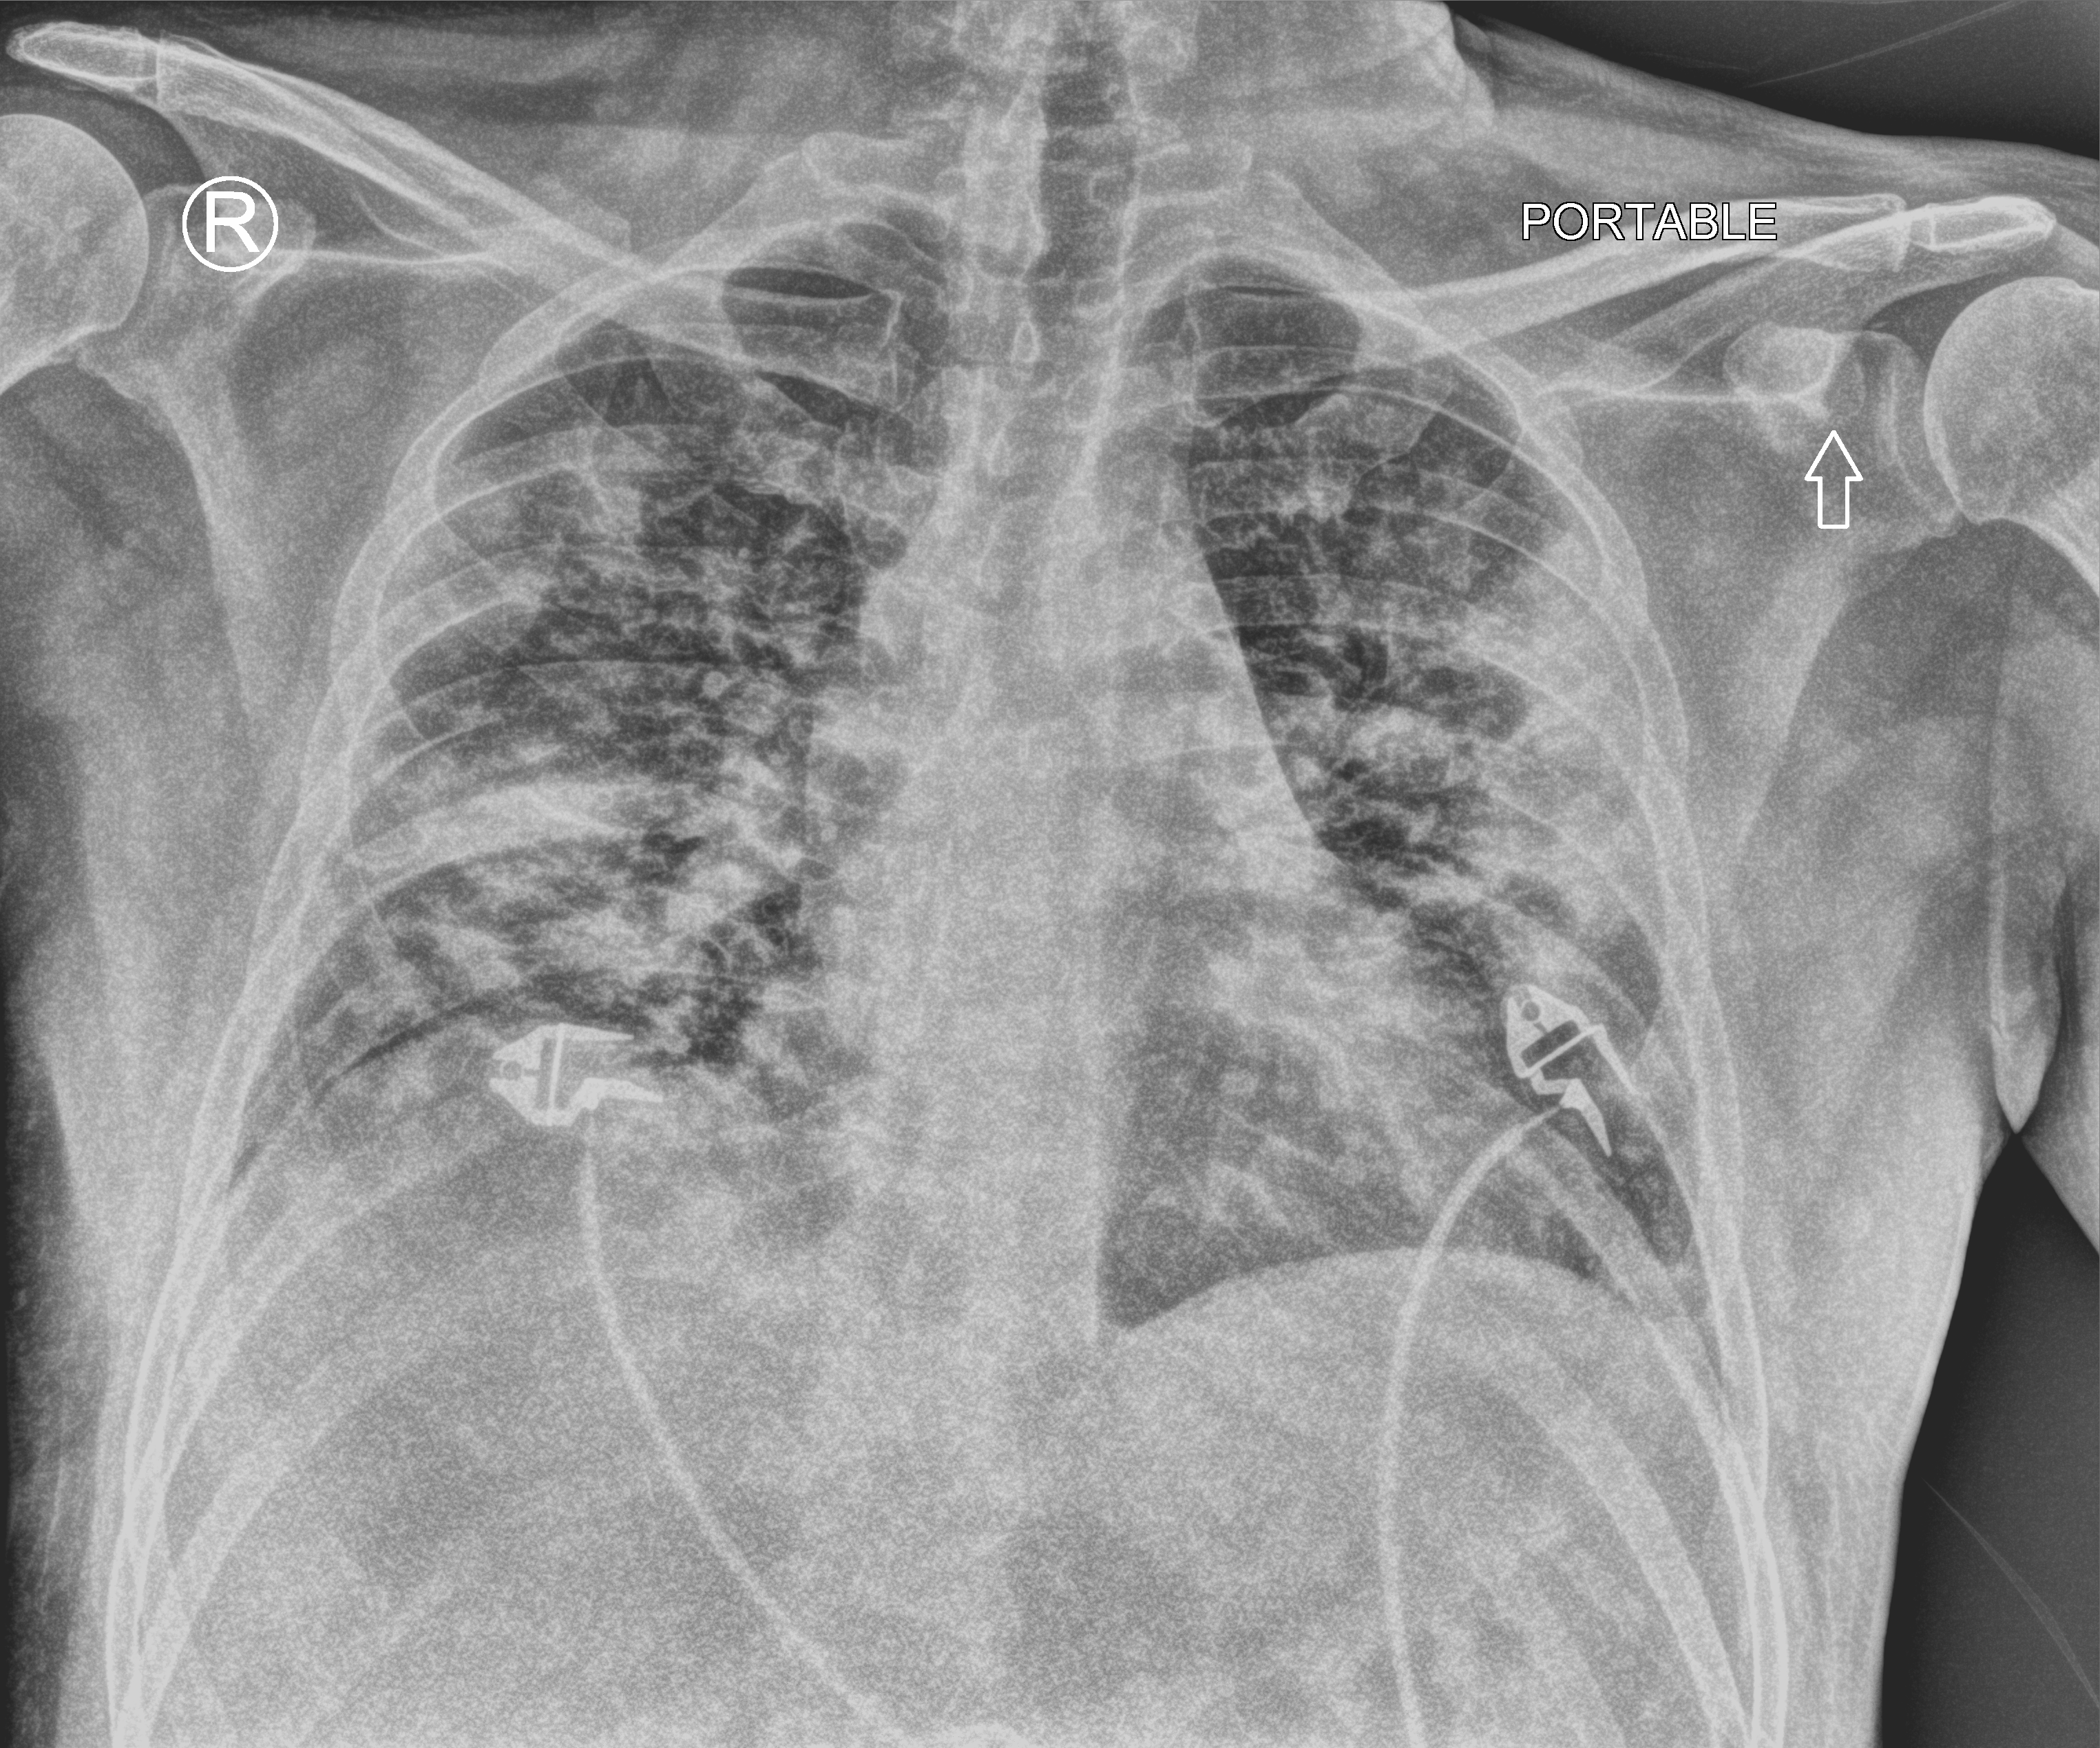
Bedside chest radiograph (computed radiography); anteroposterior (AP) projection. Patient hospitalised with COVID-19; male, aged 18–59 years.
From the hospital-stay record, not from the radiograph (when in the stay this image was taken is not recorded): mechanically ventilated during this hospital stay: no; admitted to intensive care during this hospital stay: no.